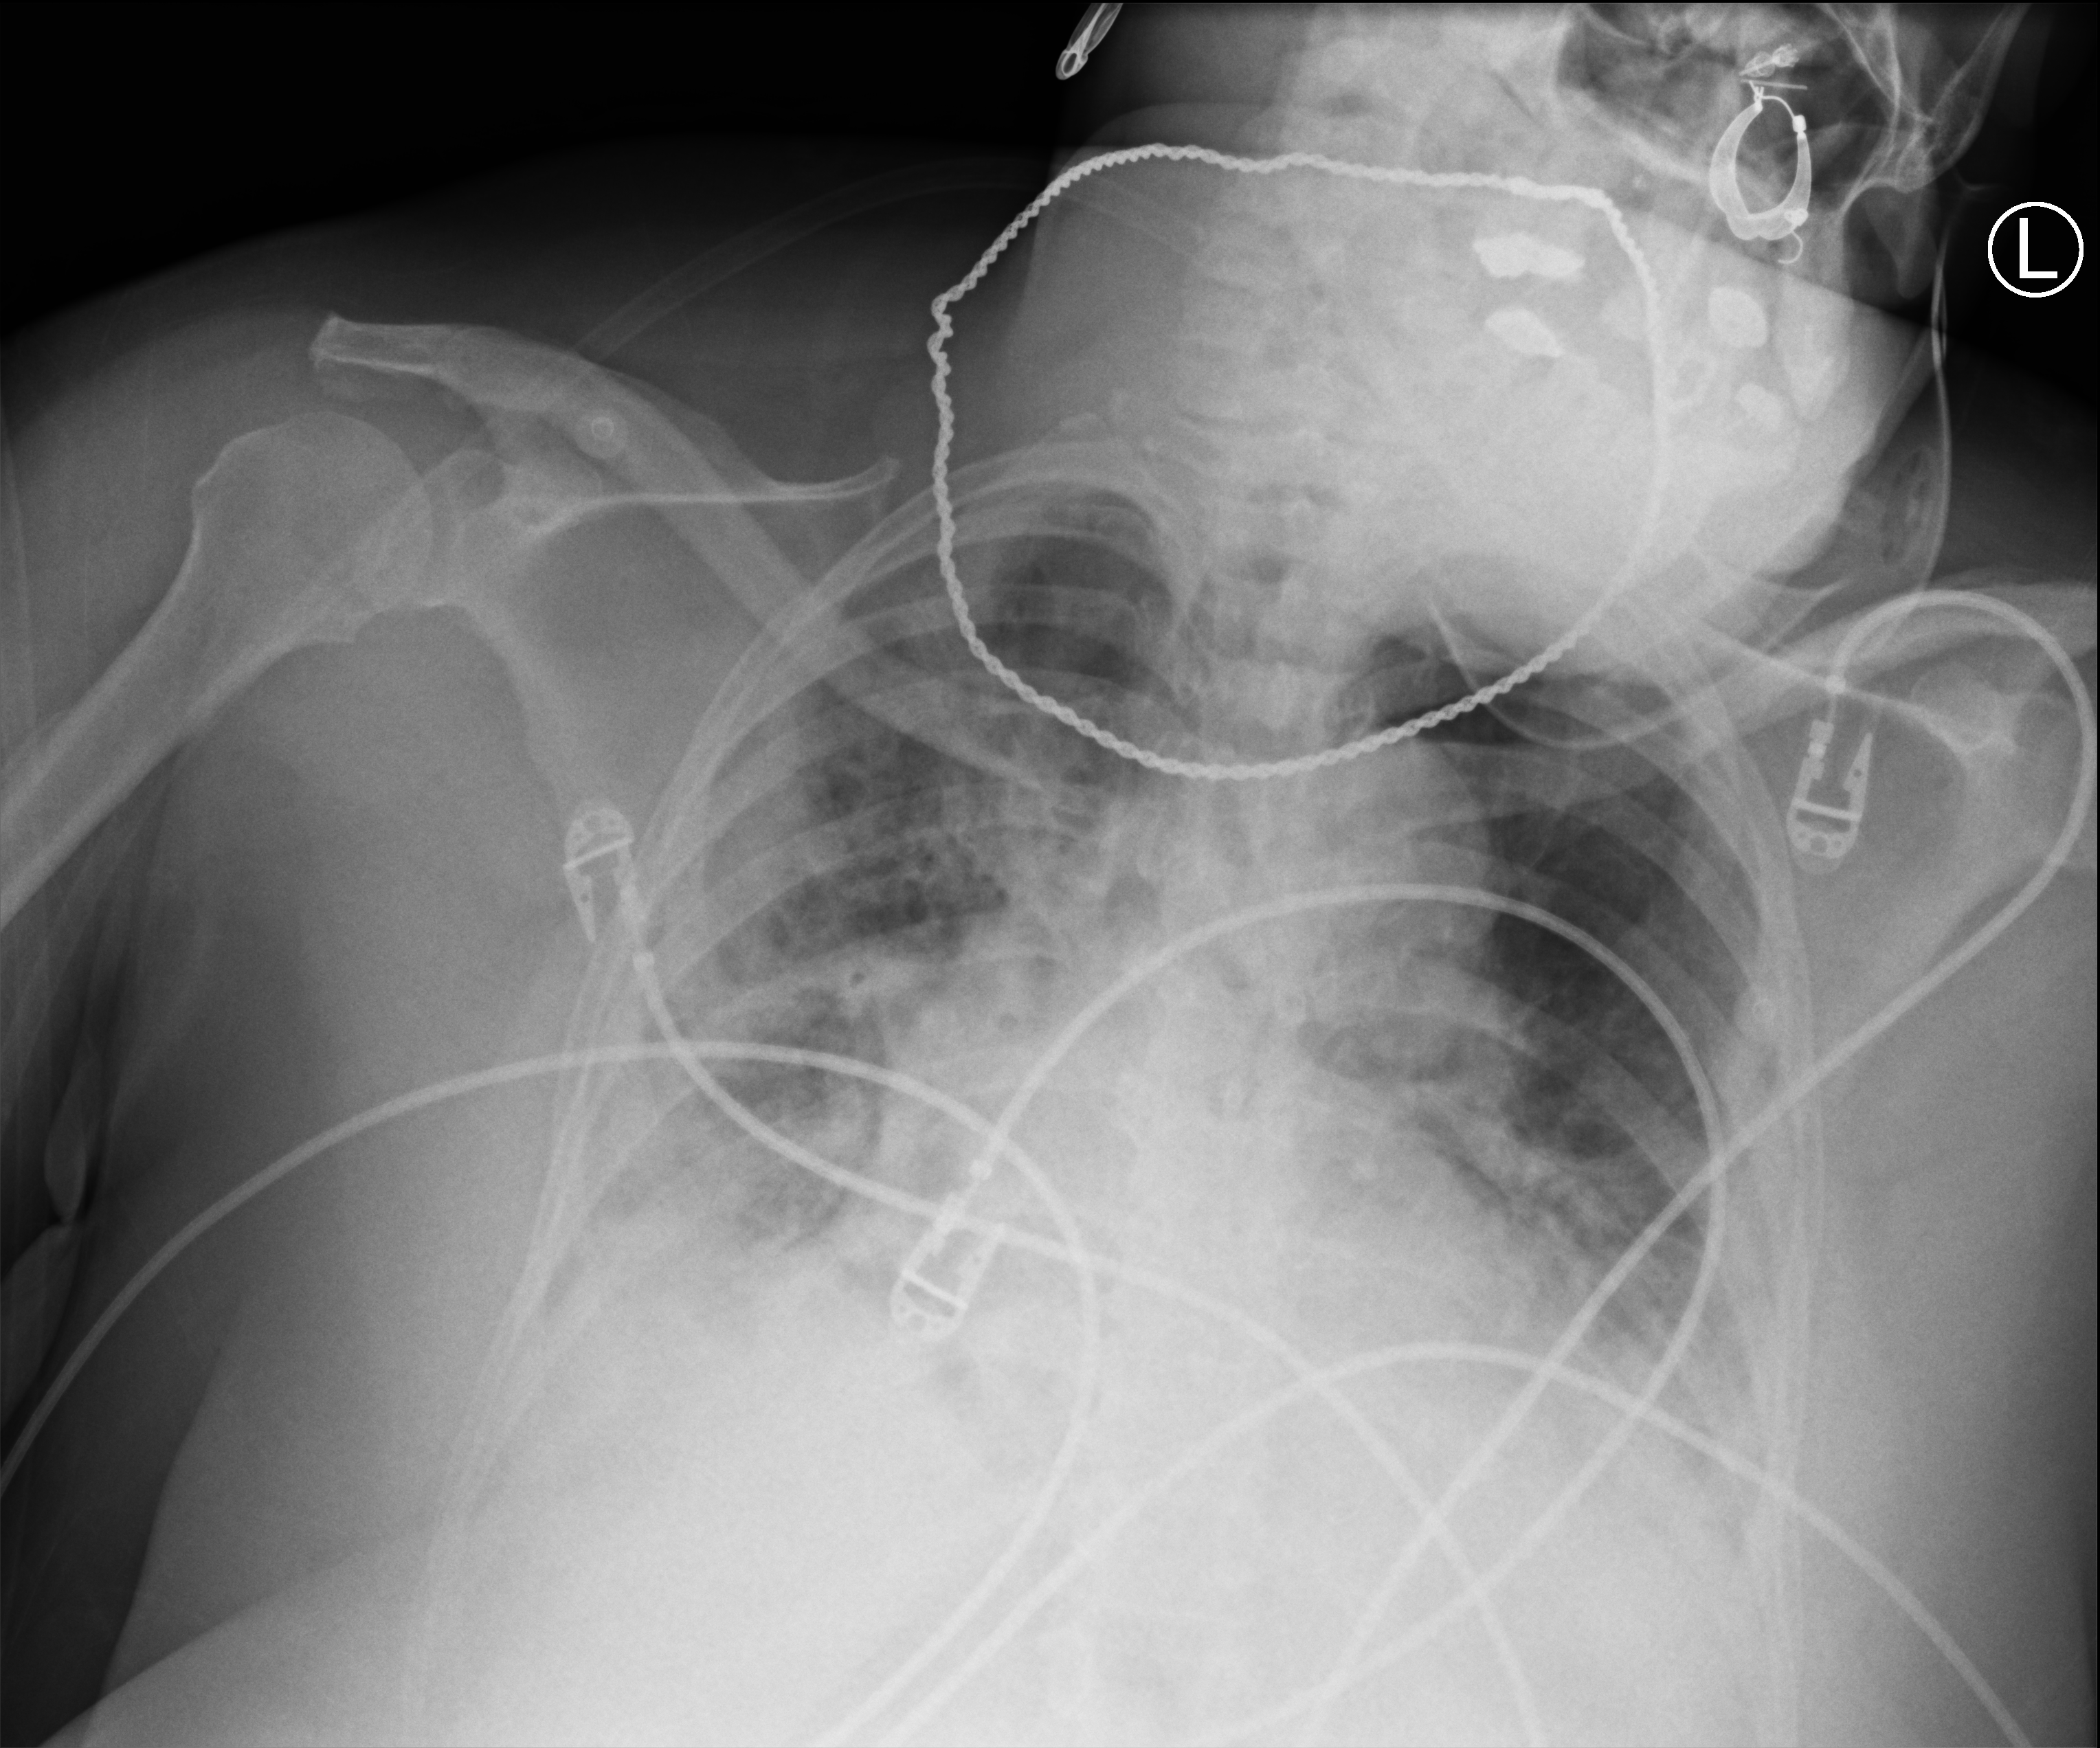
Portable chest radiograph. Female patient hospitalised with COVID-19, age 60–74 years.
Admission-level facts for this patient (not findings on this image; timing relative to this image not recorded):
- mechanically ventilated during this hospital stay: yes
- length of hospital stay: 9 days